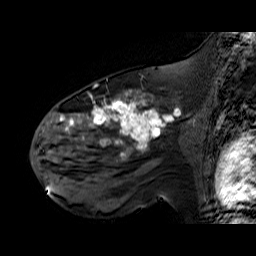
Breast MRI (dynamic contrast-enhanced), one sagittal slice; slice 38 of 60 in the series (ordered by position); dynamic contrast-enhanced series, time point 2 of 6 at this slice position (early post-contrast); 1.5 T; TE 6.3 ms, TR 32.9 ms; 4 mm slice thickness; 256 × 256 image matrix, field of view 200 × 200 mm. Female patient. Case-level facts recorded for this patient, not image findings: setting: breast cancer imaged before/during neoadjuvant chemotherapy; receptor status: HER2-positive.
Outlined on this slice (semi-automatically segmented with operator editing):
- analysis volume of interest (the breast-tissue region the enhancement analysis was run in; not a lesion): bounding box [x1, y1, x2, y2] px = [48, 92, 195, 174]
- tumour enhancement mask (voxels above the 100 % enhancement threshold inside the analysis volume of interest): [60, 92, 168, 156]